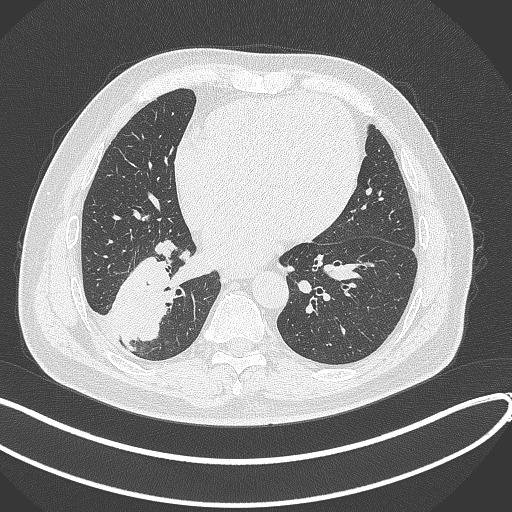
Chest CT, one axial slice. Position 135 of 360 along the scan axis. 120 kVp. Lung window (W 1500 / L -600 HU). 512 × 512 image matrix, field of view 400 × 400 mm. Male patient, age 59 years.
Outlined on this slice (bounding box drawn by a radiologist):
- lung tumour (recorded histology: adenocarcinoma): bounding box [x1, y1, x2, y2] px = [108, 255, 171, 343]